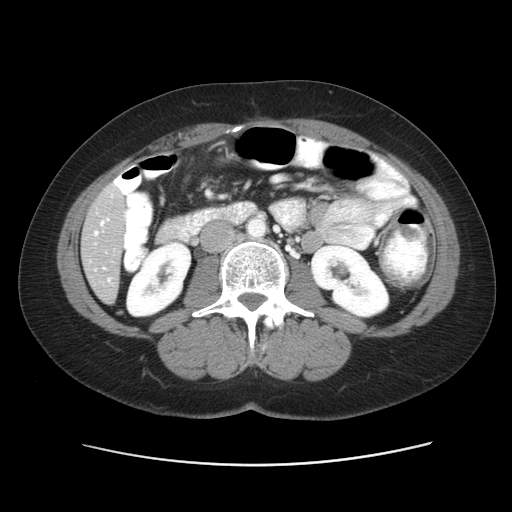
Contrast-enhanced abdominal CT, one axial slice; position 17 of 52 along the scan axis; reconstruction kernel STANDARD; 120 kVp; intravenous contrast given; soft-tissue window (W 400 / L 40 HU); 5 mm slice thickness; 512 × 512 image matrix, field of view 362 × 362 mm. Female patient, age 48 years. Case-level facts recorded for this patient, not image findings: diagnosis: colorectal cancer liver metastases, imaged before liver resection; multiple liver metastases: yes; largest metastasis: 4.5 cm; disease in both lobes: yes.
Annotated regions visible in this slice (outlined manually by an expert reader):
- hepatic veins: bounding box <95,219,110,282> (left, top, right, bottom; pixels)
- liver: <83,187,124,302>